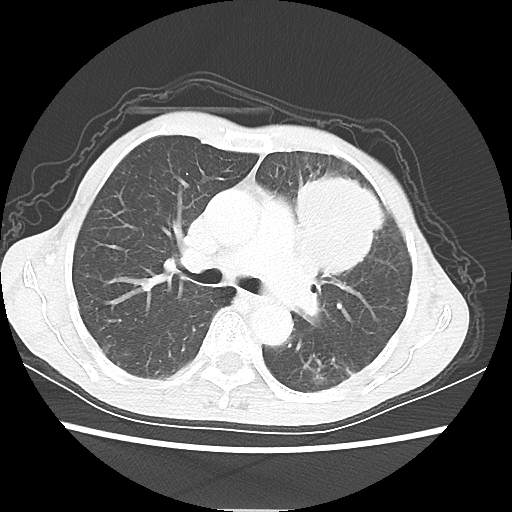
Chest CT, one axial slice; position 37 of 56 along the scan axis; reconstruction kernel LUNG; lung window (W 1500 / L -600 HU); 512 × 512 image matrix, field of view 331 × 331 mm. Patient: female, 60 years. From the clinical record (not read from this slice): clinical TNM (as recorded): T4 N1 M0.
Outlined on this slice (rectangle marked by the reading radiologist):
- lung tumour (recorded histology: adenocarcinoma): box from (x=286, y=169) to (x=397, y=283) px